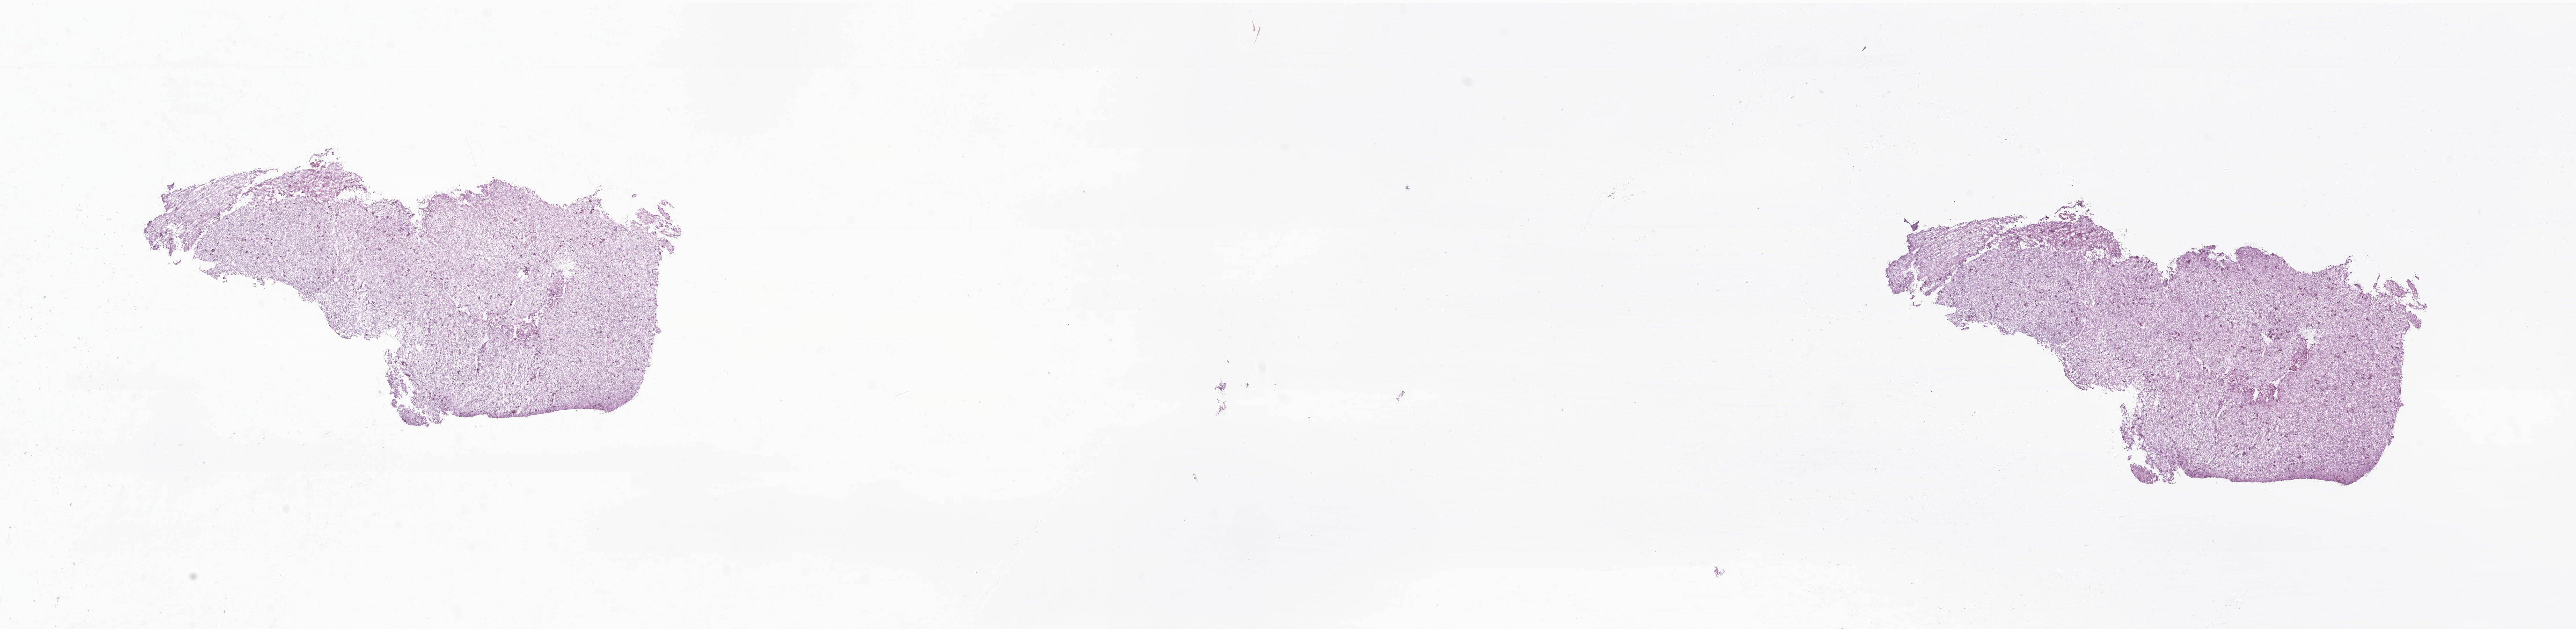
Whole-slide image, H&E stain of tumor tissue from the brain — whole scanned area (about 34.1 x 8.3 mm) shown as a low-resolution overview. Frozen section (OCT-embedded). Female patient, age 780 days (about 2.1 years).
* diagnosis: Neoplasm, malignant